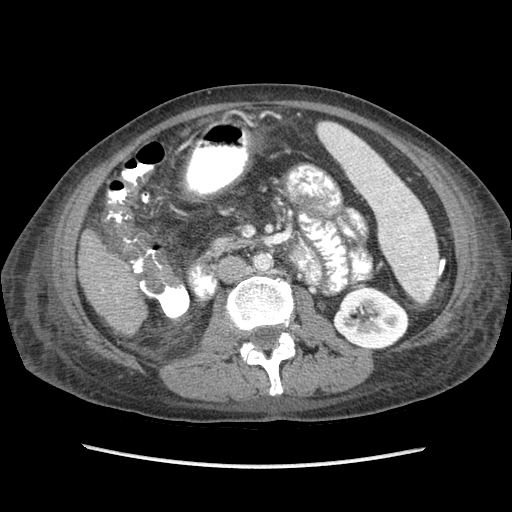
Contrast-enhanced abdominal CT (liver protocol), one axial slice; reconstruction kernel STANDARD; soft-tissue window (W 400 / L 40 HU); 512 × 512 image matrix, field of view 340 × 340 mm. From the clinical record (not read from this slice): diagnosis: hepatocellular carcinoma (patient treated with transarterial chemoembolisation; whether this scan precedes or follows treatment is not stated here); TNM stage (as recorded): Stage-IIIB; Child-Pugh class: A; tumour differentiation: no biopsy.
Outlined on this slice (semi-automatically segmented with operator editing):
- liver parenchyma outside the tumour (the mass and vessels are separate outlines, so this box may not span the whole liver): bounding box (x1, y1, x2, y2) in pixels: (78, 229, 146, 332)